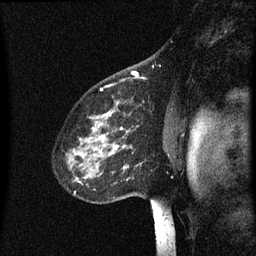
Breast MRI (dynamic contrast-enhanced), one sagittal slice. Position 47 of 60 along the scan axis. Dynamic contrast-enhanced series, image 2 of 3 at this slice position (ordered by acquisition). 1.5 T. TE 4.2 ms, TR 8 ms. 2 mm slice thickness. 256 × 256 image matrix. Female patient, age 60 years.
Annotated regions visible in this slice (semi-automatically segmented with operator editing):
- analysis volume of interest (the breast-tissue region the enhancement analysis was run in; not a lesion): box from (x=67, y=102) to (x=144, y=197) px
- tumour enhancement mask (voxels above the 70 % enhancement threshold inside the analysis volume of interest): (x=95, y=114)–(x=129, y=169)